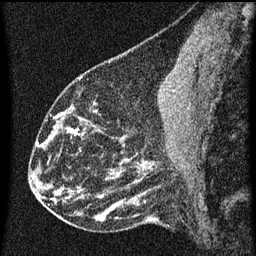
Breast MRI (dynamic contrast-enhanced), one sagittal slice; slice 28 of 60 in the series (ordered by position); dynamic contrast-enhanced series, image 2 of 3 at this slice position (ordered by acquisition); 1.5 T; TE 4.2 ms, TR 8 ms; 2 mm slice thickness; 256 × 256 image matrix, field of view 180 × 180 mm. Female patient, age 43 years.
Structures marked on this image (semi-automatic segmentation, software-assisted and operator-edited):
- analysis volume of interest (the breast-tissue region the enhancement analysis was run in; not a lesion): box from (x=55, y=104) to (x=101, y=153) px
- tumour enhancement mask (voxels above the 70 % enhancement threshold inside the analysis volume of interest): (x=63, y=112)–(x=97, y=135)